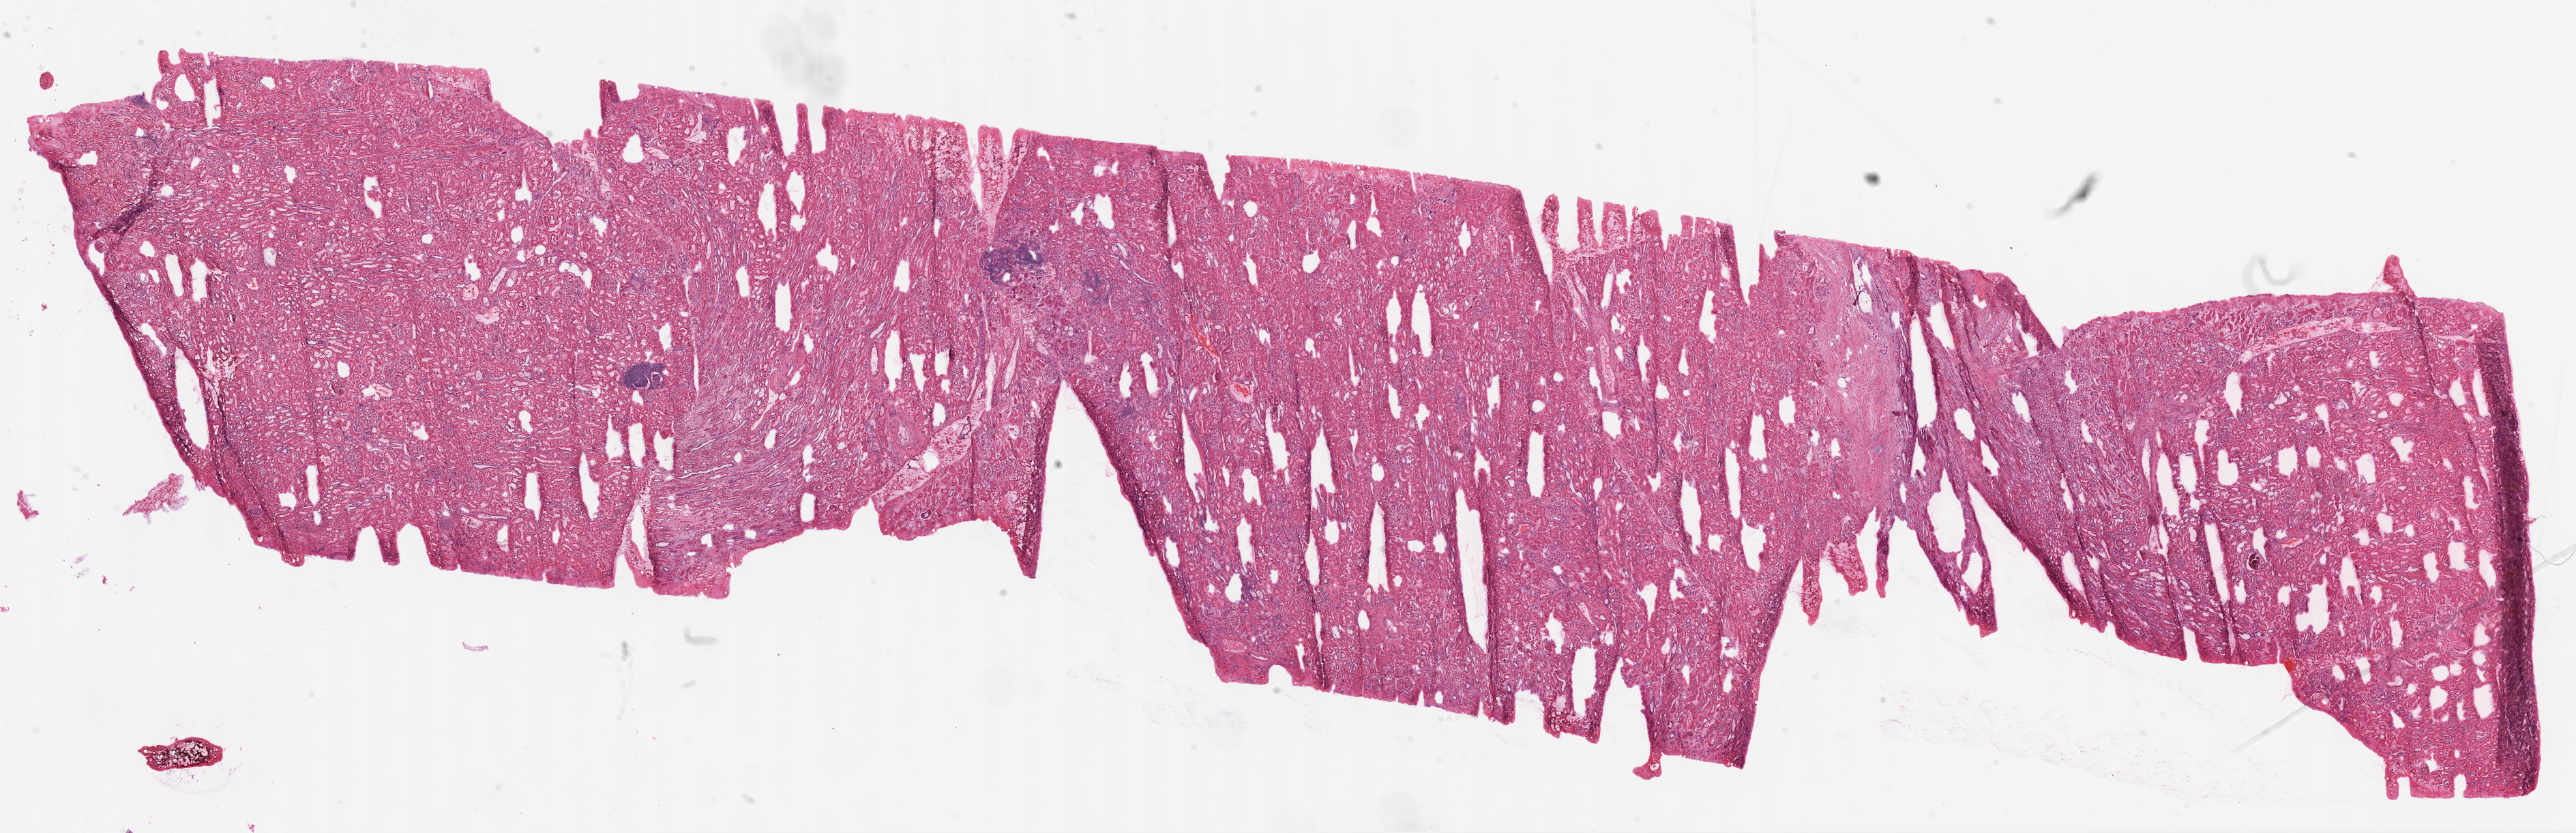
Whole-slide histology image, H&E — shown as a low-resolution overview of the whole scanned area (about 30.5 x 9.8 mm, acquisition: 20x scan), frozen section from the top of the tissue portion, solid tissue normal (non-tumour tissue) sample from the kidney. Male, age 62 years at initial diagnosis.
This section: solid tissue normal sample (biorepository sample class). Patient diagnosis: Clear cell adenocarcinoma, NOS.